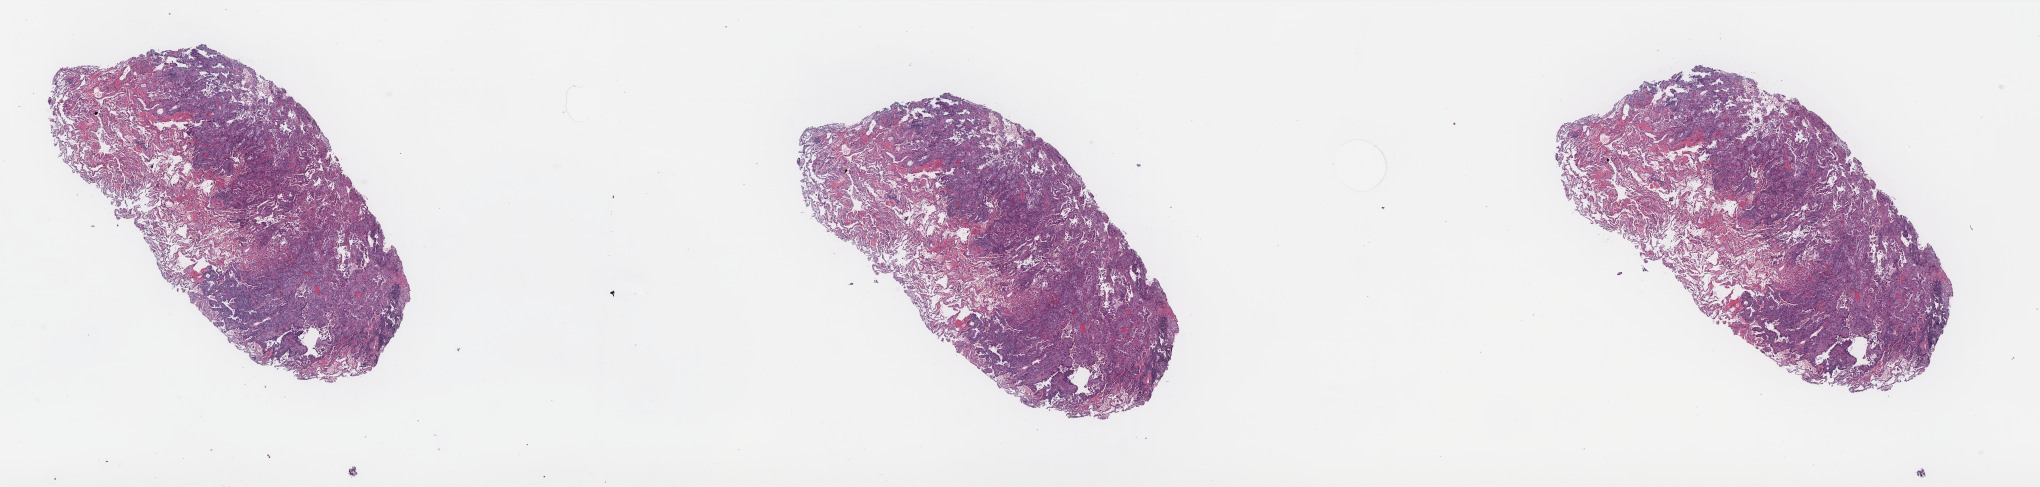
Hematoxylin and eosin (H&E) stained whole-slide image, a low-resolution overview of the entire scanned area, about 32.7 x 7.8 mm; formalin-fixed paraffin-embedded (FFPE) diagnostic section; primary tumour sample from the lung. Patient: female, age at initial diagnosis 73 years.
AJCC pathologic stage: IA (7th edition). Histologic diagnosis: Adenocarcinoma, NOS (upper lobe, lung).